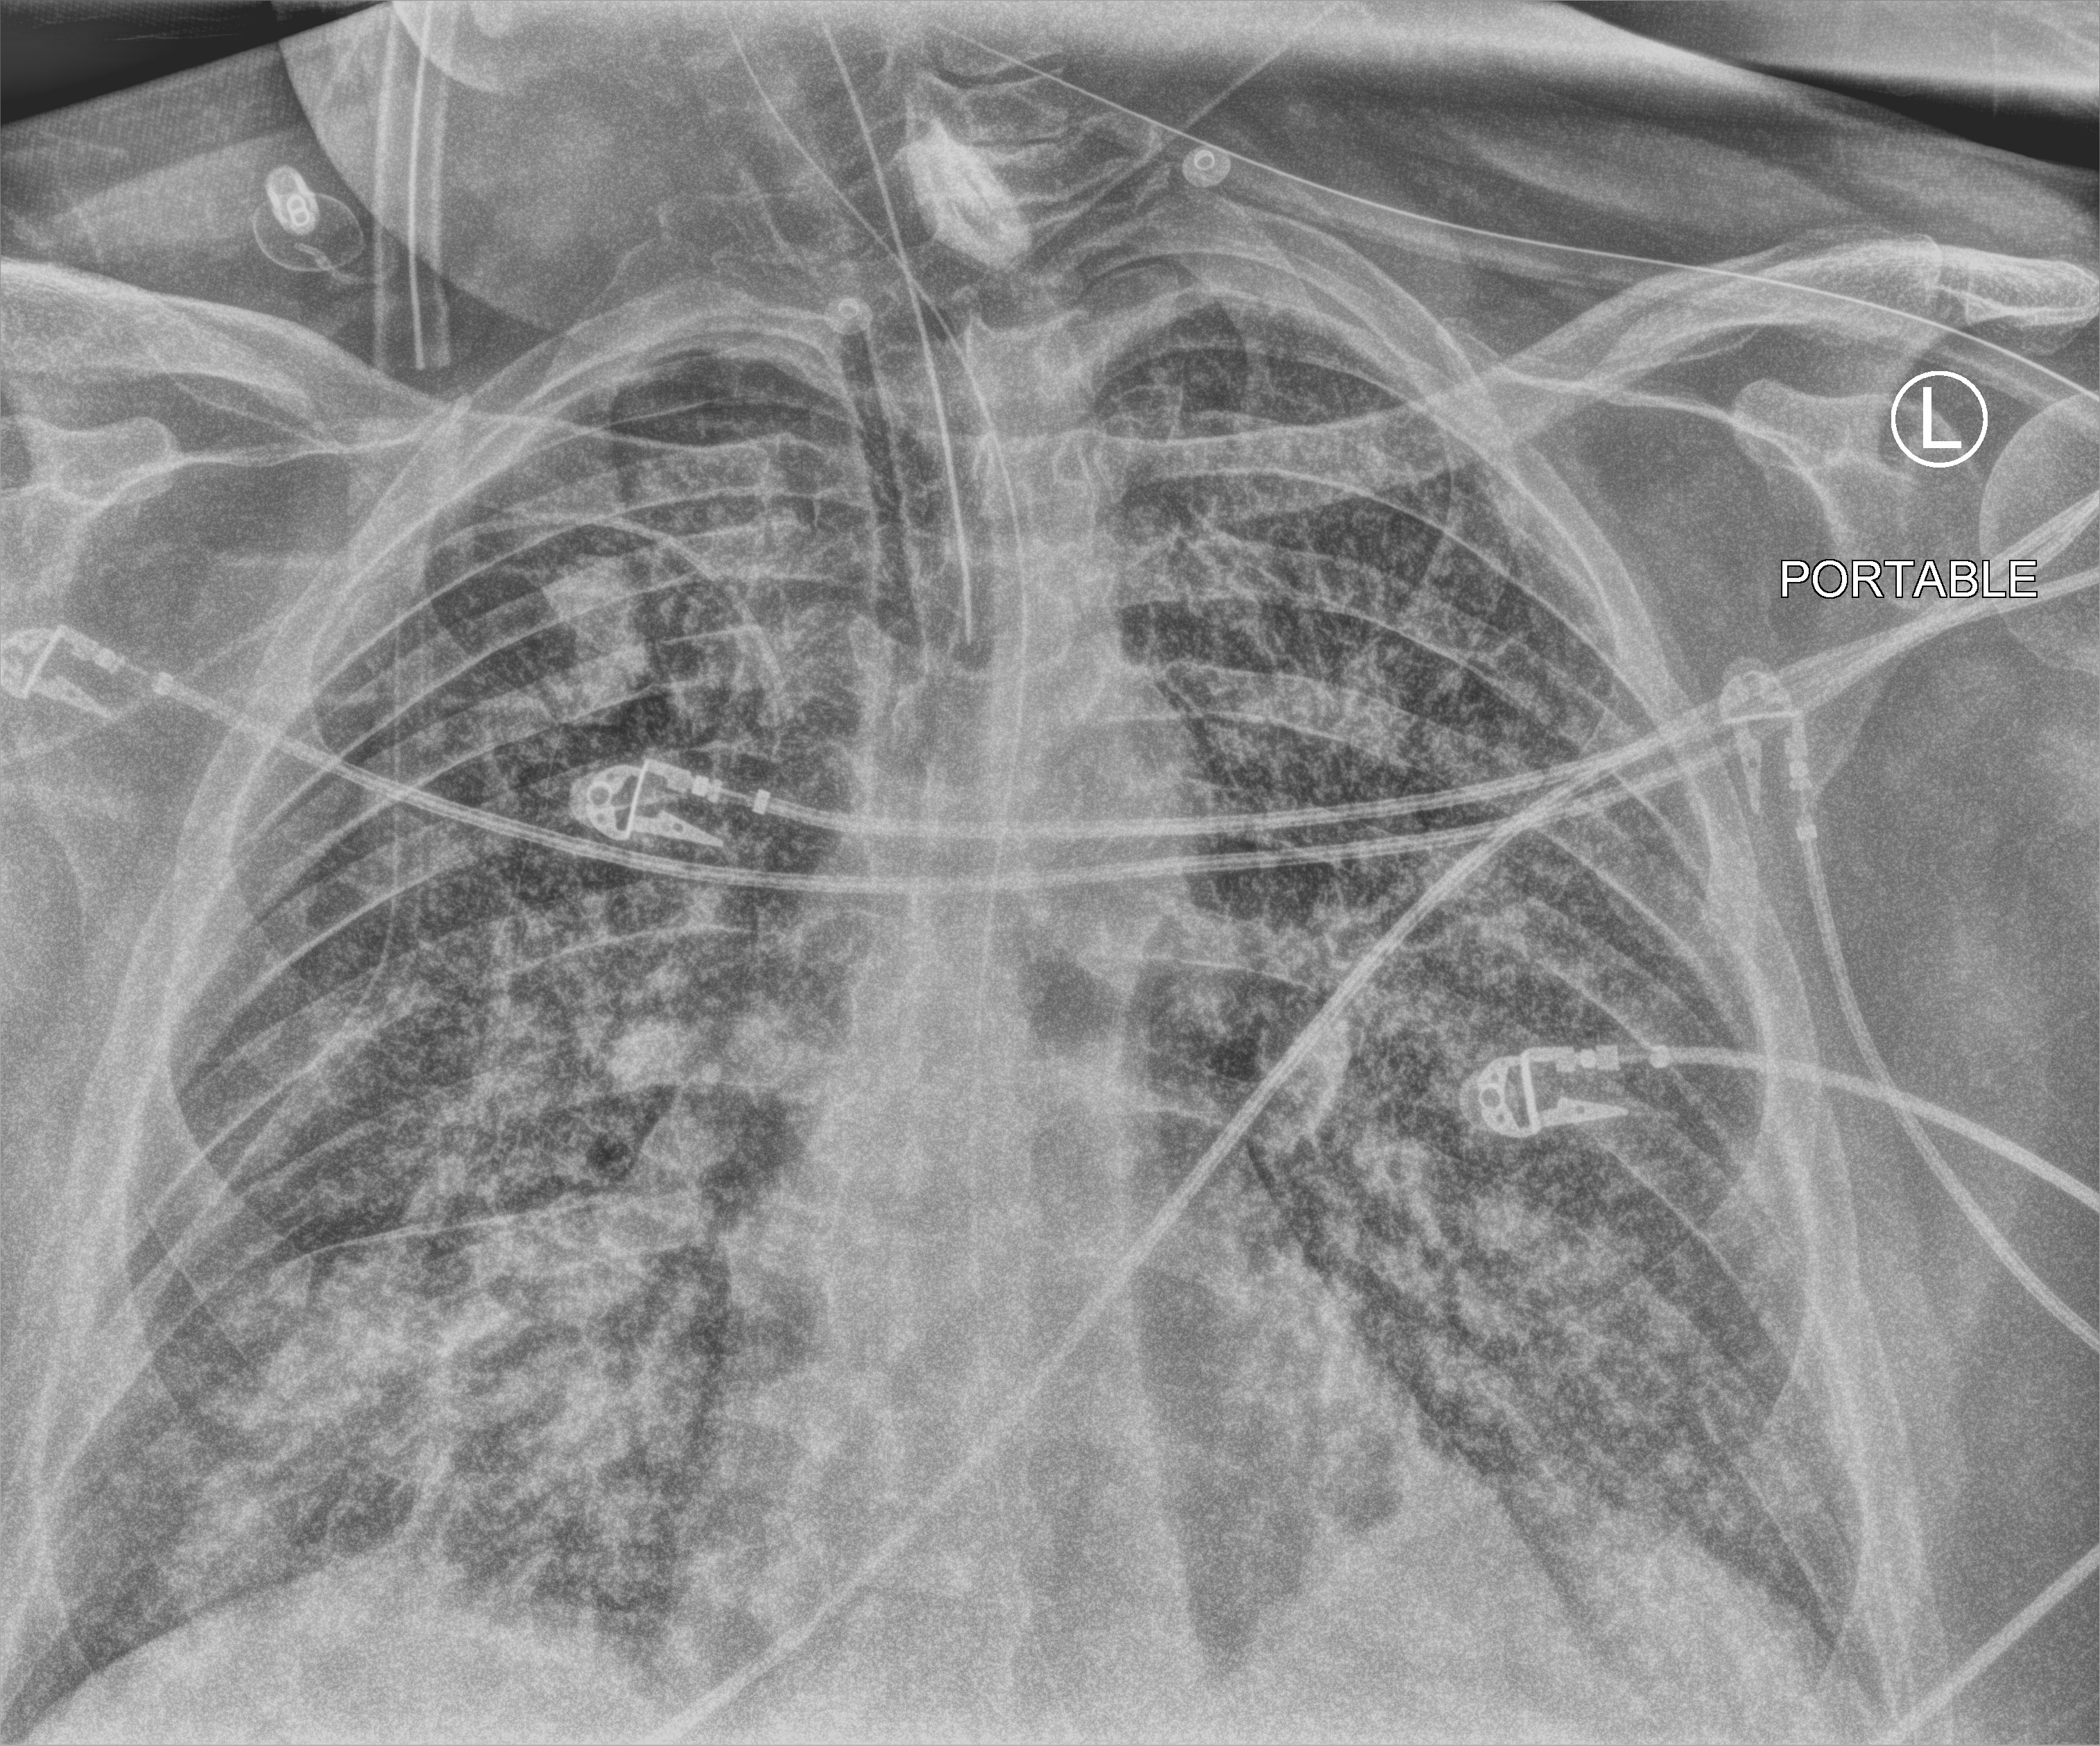
Portable chest radiograph; anteroposterior (AP) projection. Patient hospitalised with COVID-19; male, aged 60–74 years.
From the hospital-stay record, not from the radiograph (when in the stay this image was taken is not recorded): length of hospital stay: 13 days.